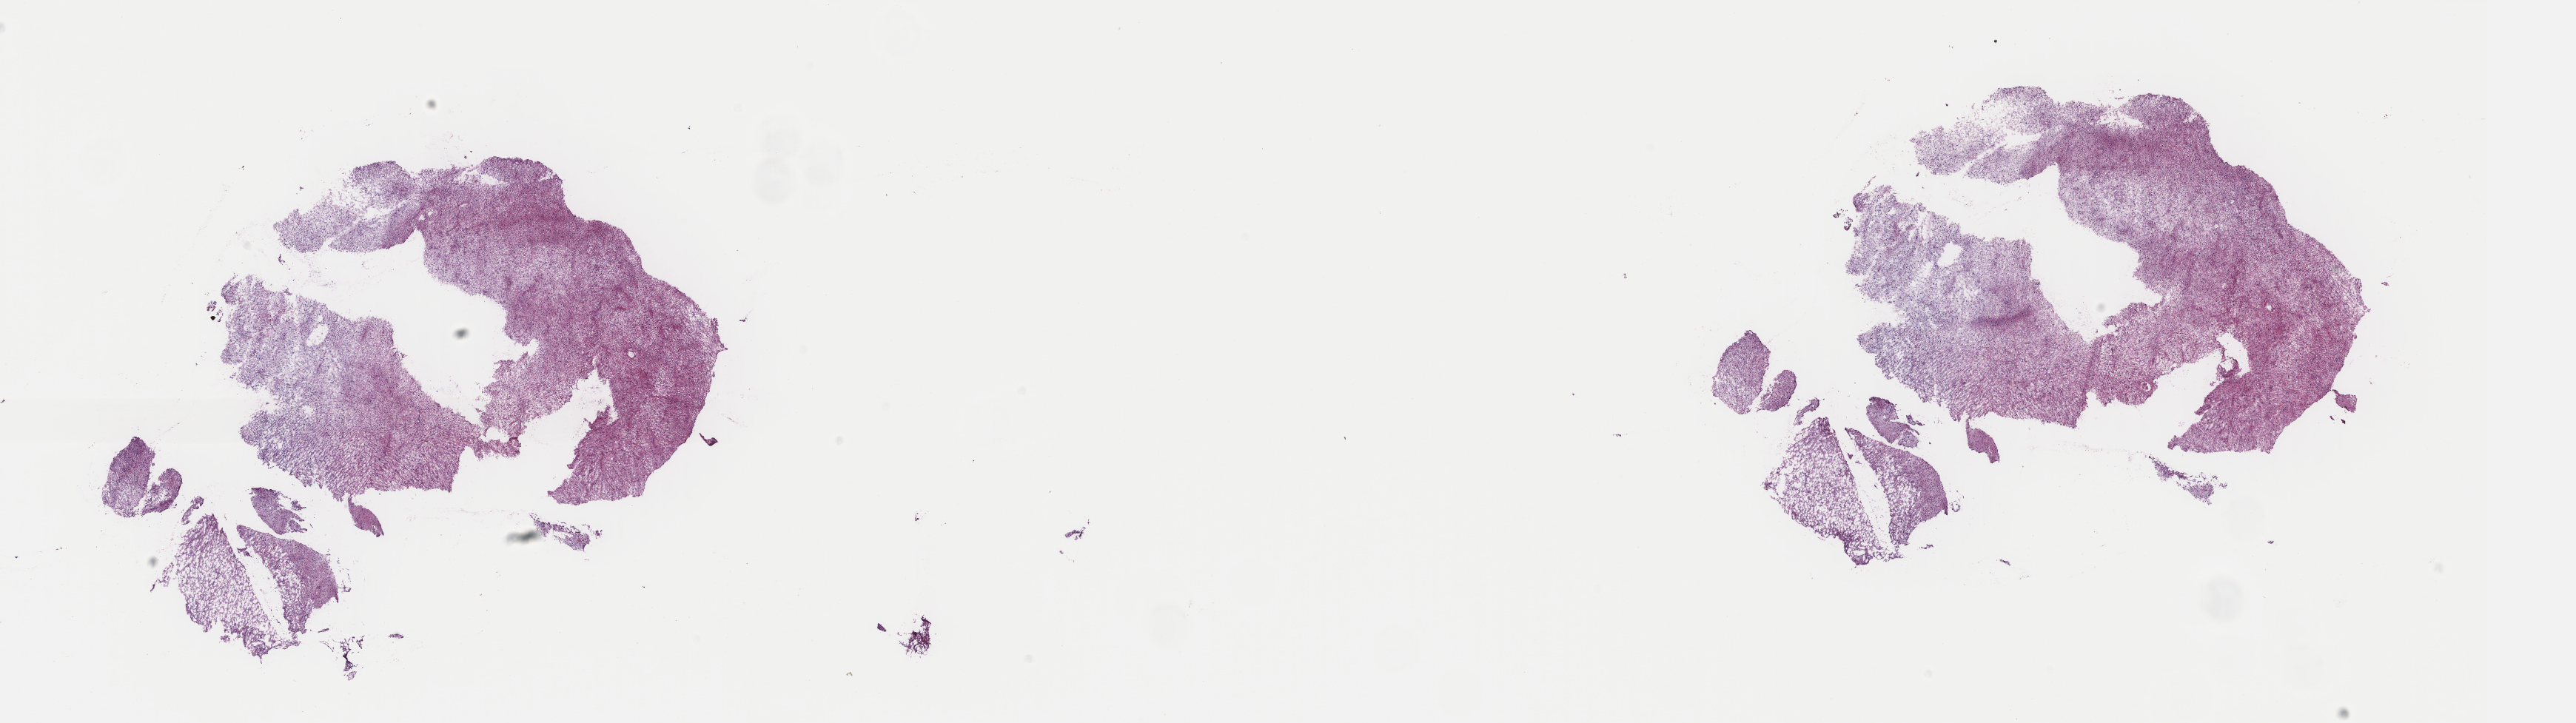
H&E-stained whole-slide image, a low-resolution overview of the entire scanned area, about 27.6 x 7.8 mm (slide scanned at 40x), frozen section, primary tumour sample from the brain. Male, age 32 years at initial diagnosis. Histologic grade: G2 (moderately differentiated). Composition of this section per pathologist review: tumour cells 45%, tumour nuclei 90%, normal cells 5%, stromal cells 50%, necrosis 0%. Infiltration values recorded for this section: lymphocyte infiltration 0%, monocyte infiltration 0%, neutrophil infiltration 0%.
• pathologic diagnosis: Mixed glioma (cerebrum)